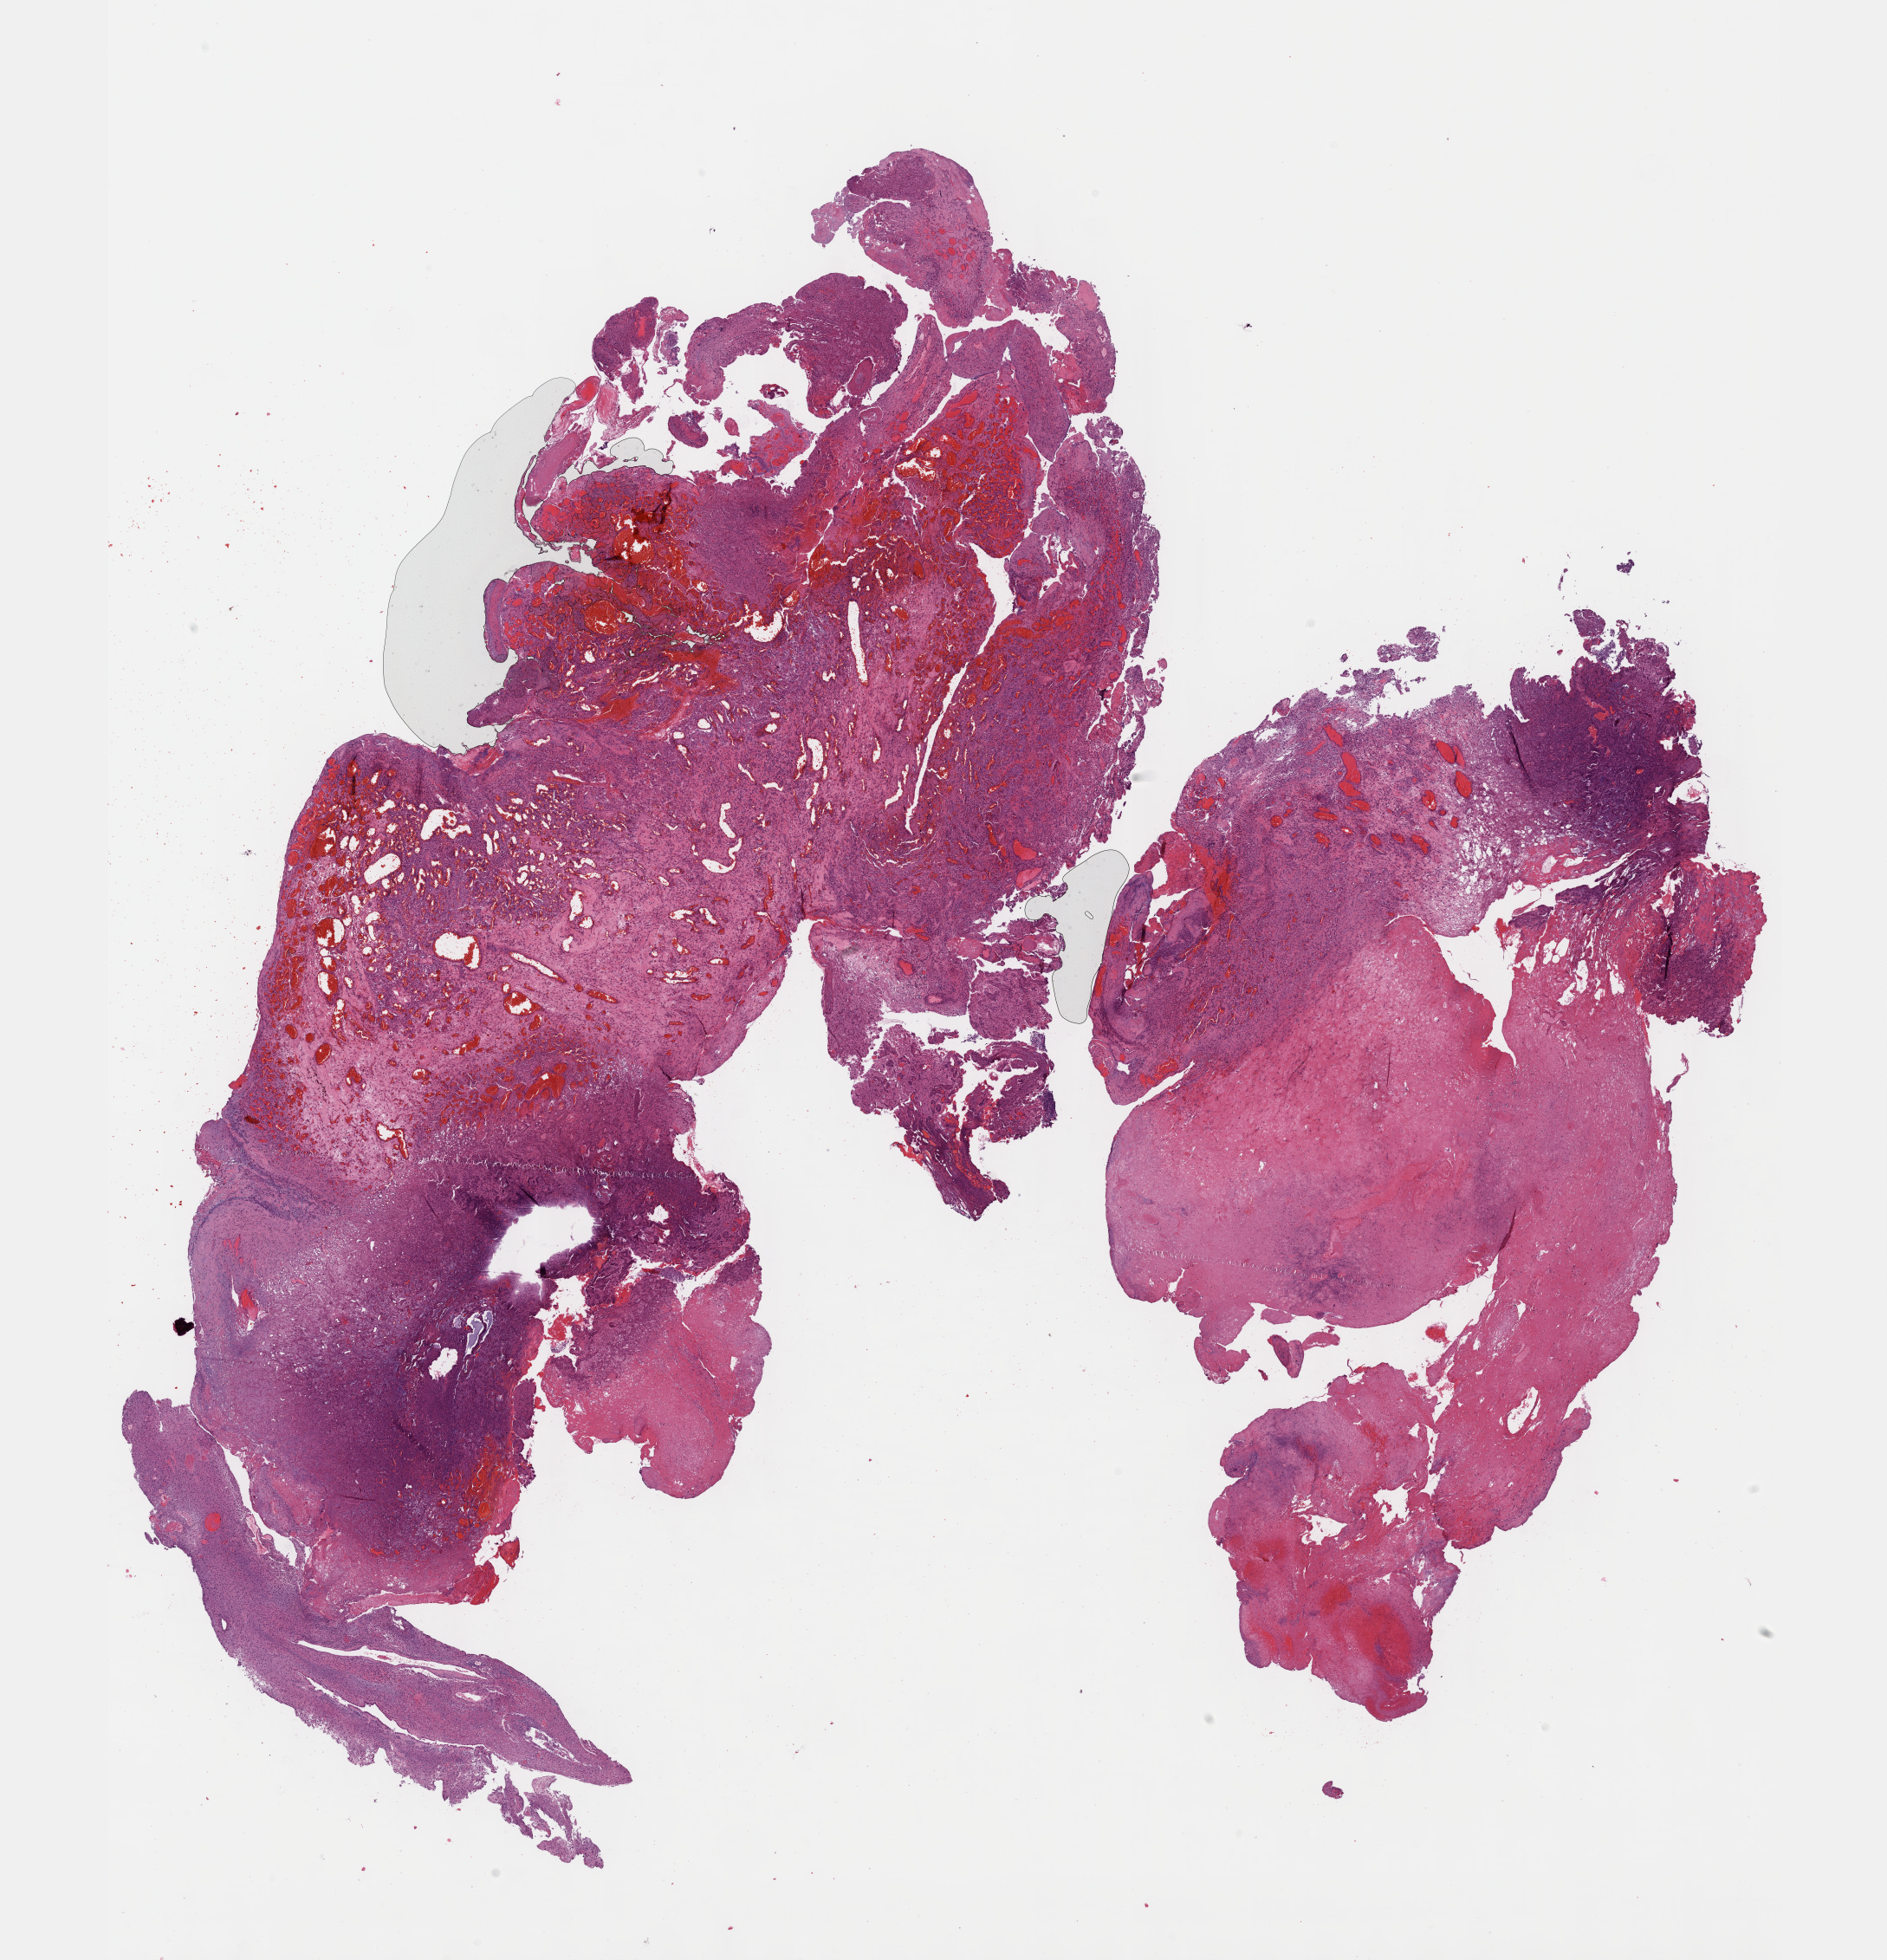
Whole-slide histology image, H&E — low-resolution overview of the scanned area, about 17.6 x 18.3 mm. Formalin-fixed paraffin-embedded (FFPE) diagnostic section. Brain, primary tumour sample. Male, age 66 years at initial diagnosis. Histologic grade: G3 (poorly differentiated).
Diagnosis: Oligodendroglioma, anaplastic.